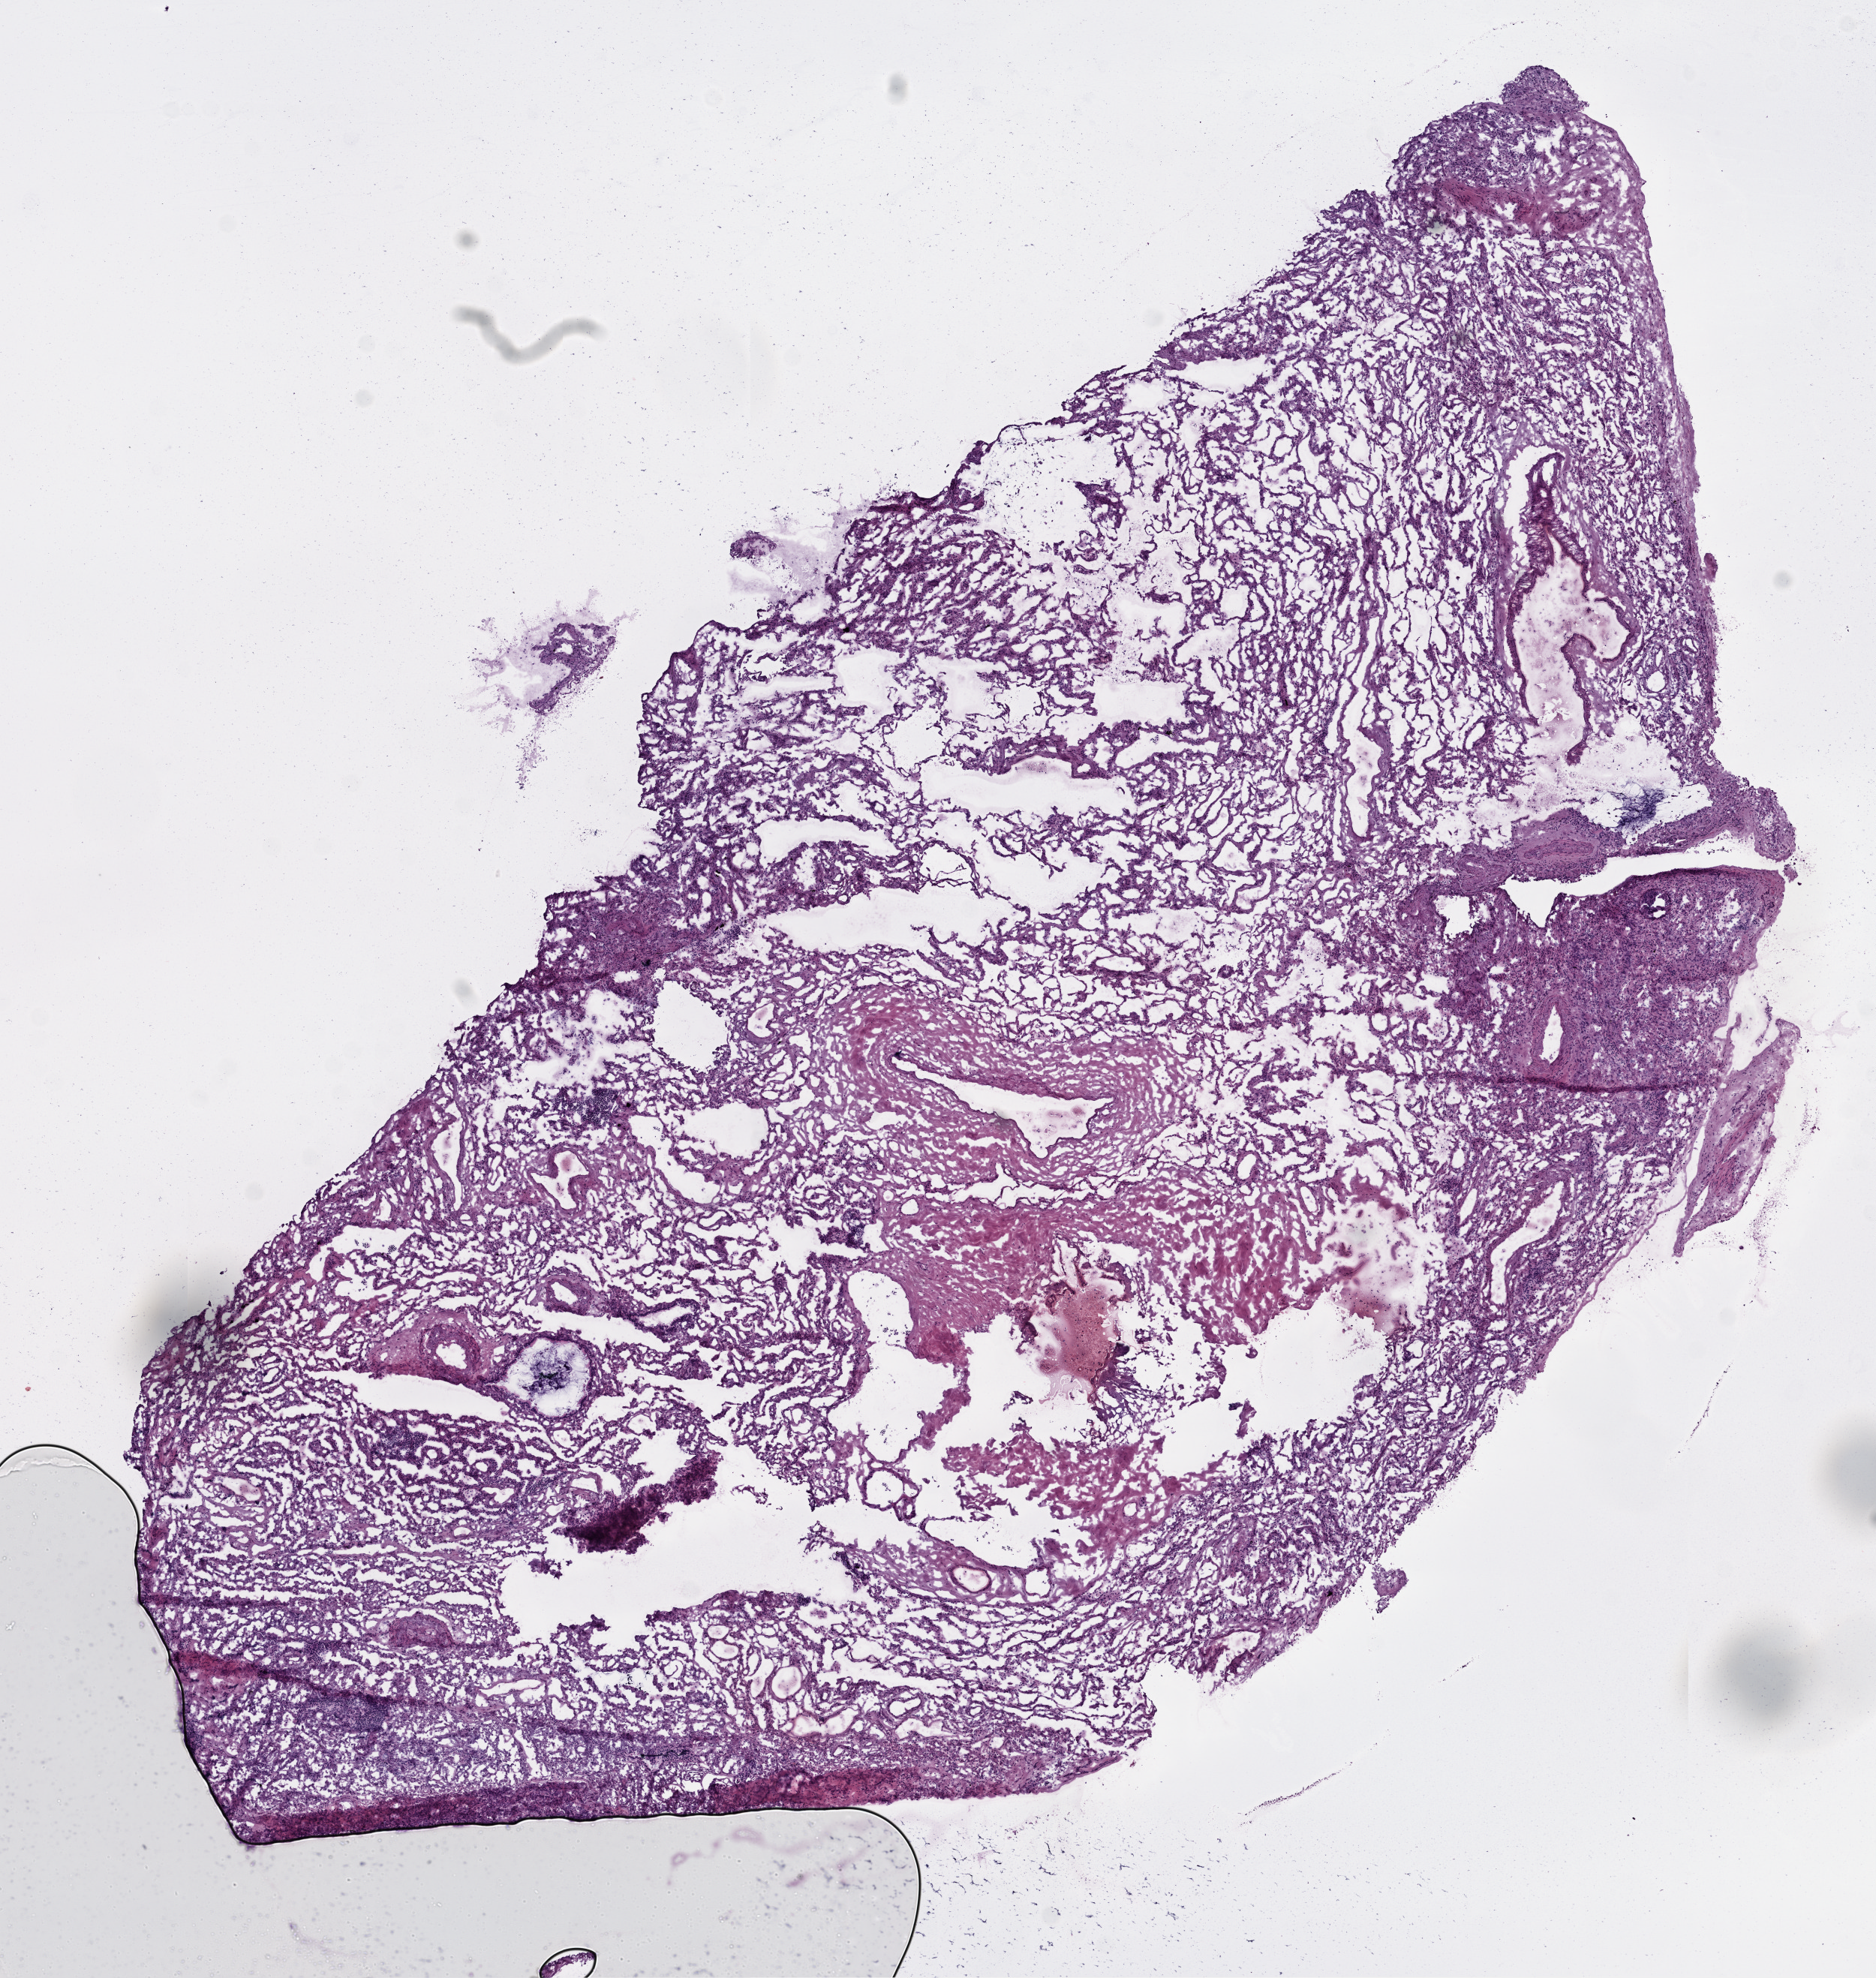
Whole-slide histology image, H&E-stained — whole scanned area (about 10.0 x 10.6 mm) shown as a low-resolution overview, frozen section from the top of the tissue portion, solid tissue normal (non-tumour tissue) sample from the lung. Female patient; age at initial diagnosis 79 years.
This section: solid tissue normal (non-tumour) sample from the same patient. Patient diagnosis: Papillary adenocarcinoma, NOS (upper lobe, lung).